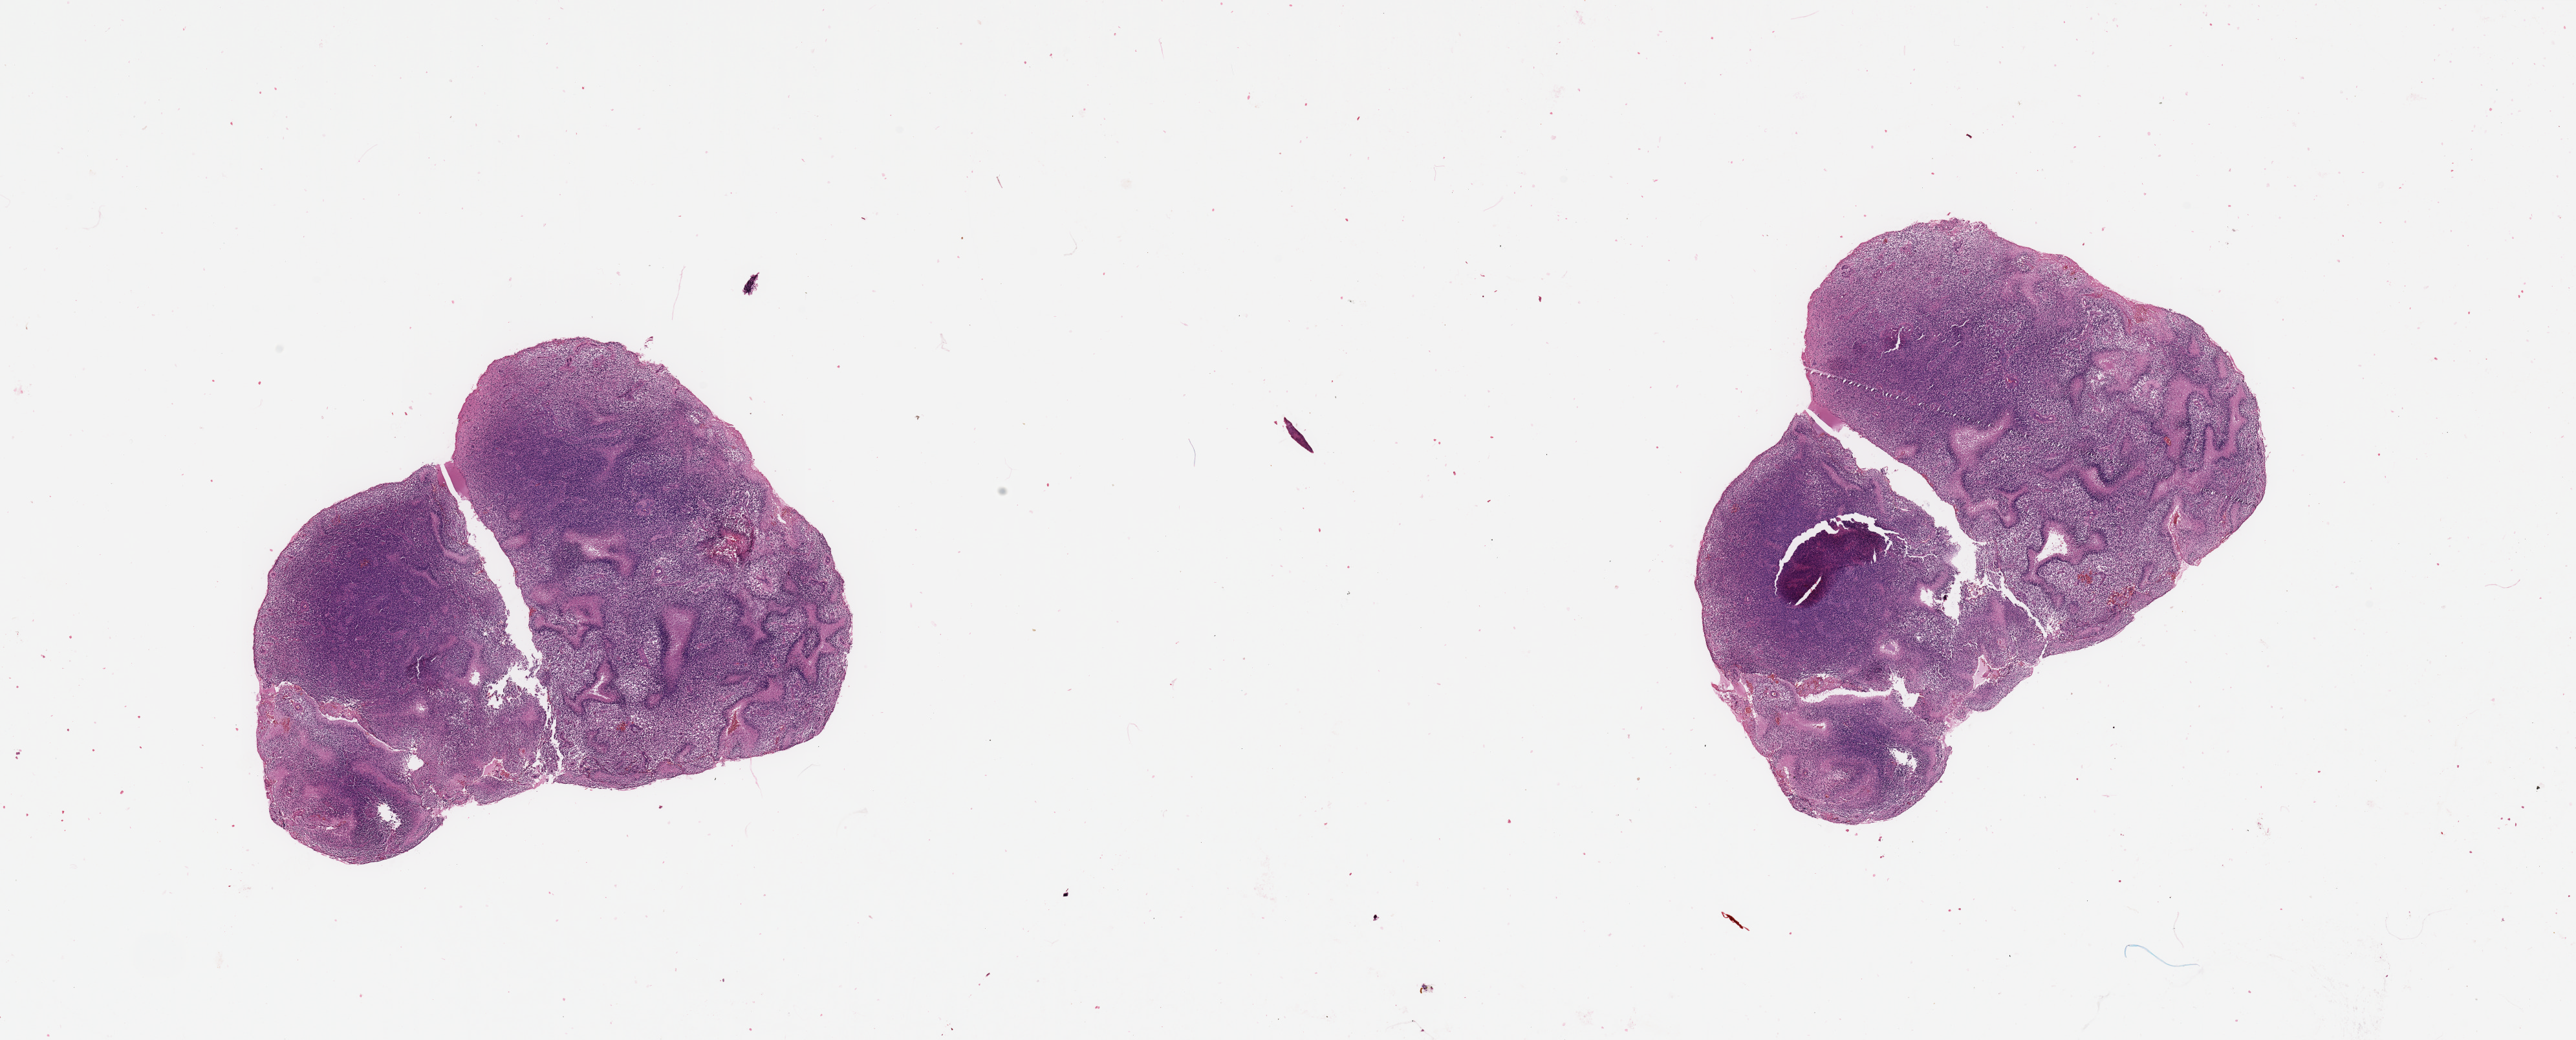
H&E whole-slide image — shown as a low-resolution overview of the whole scanned area (about 31.5 x 12.7 mm, from a 20x scan), brain, tumour tissue. Female, 68 y/o.
Histologic diagnosis: Glioblastoma. Primary tumour site (as recorded): parietal lobe.